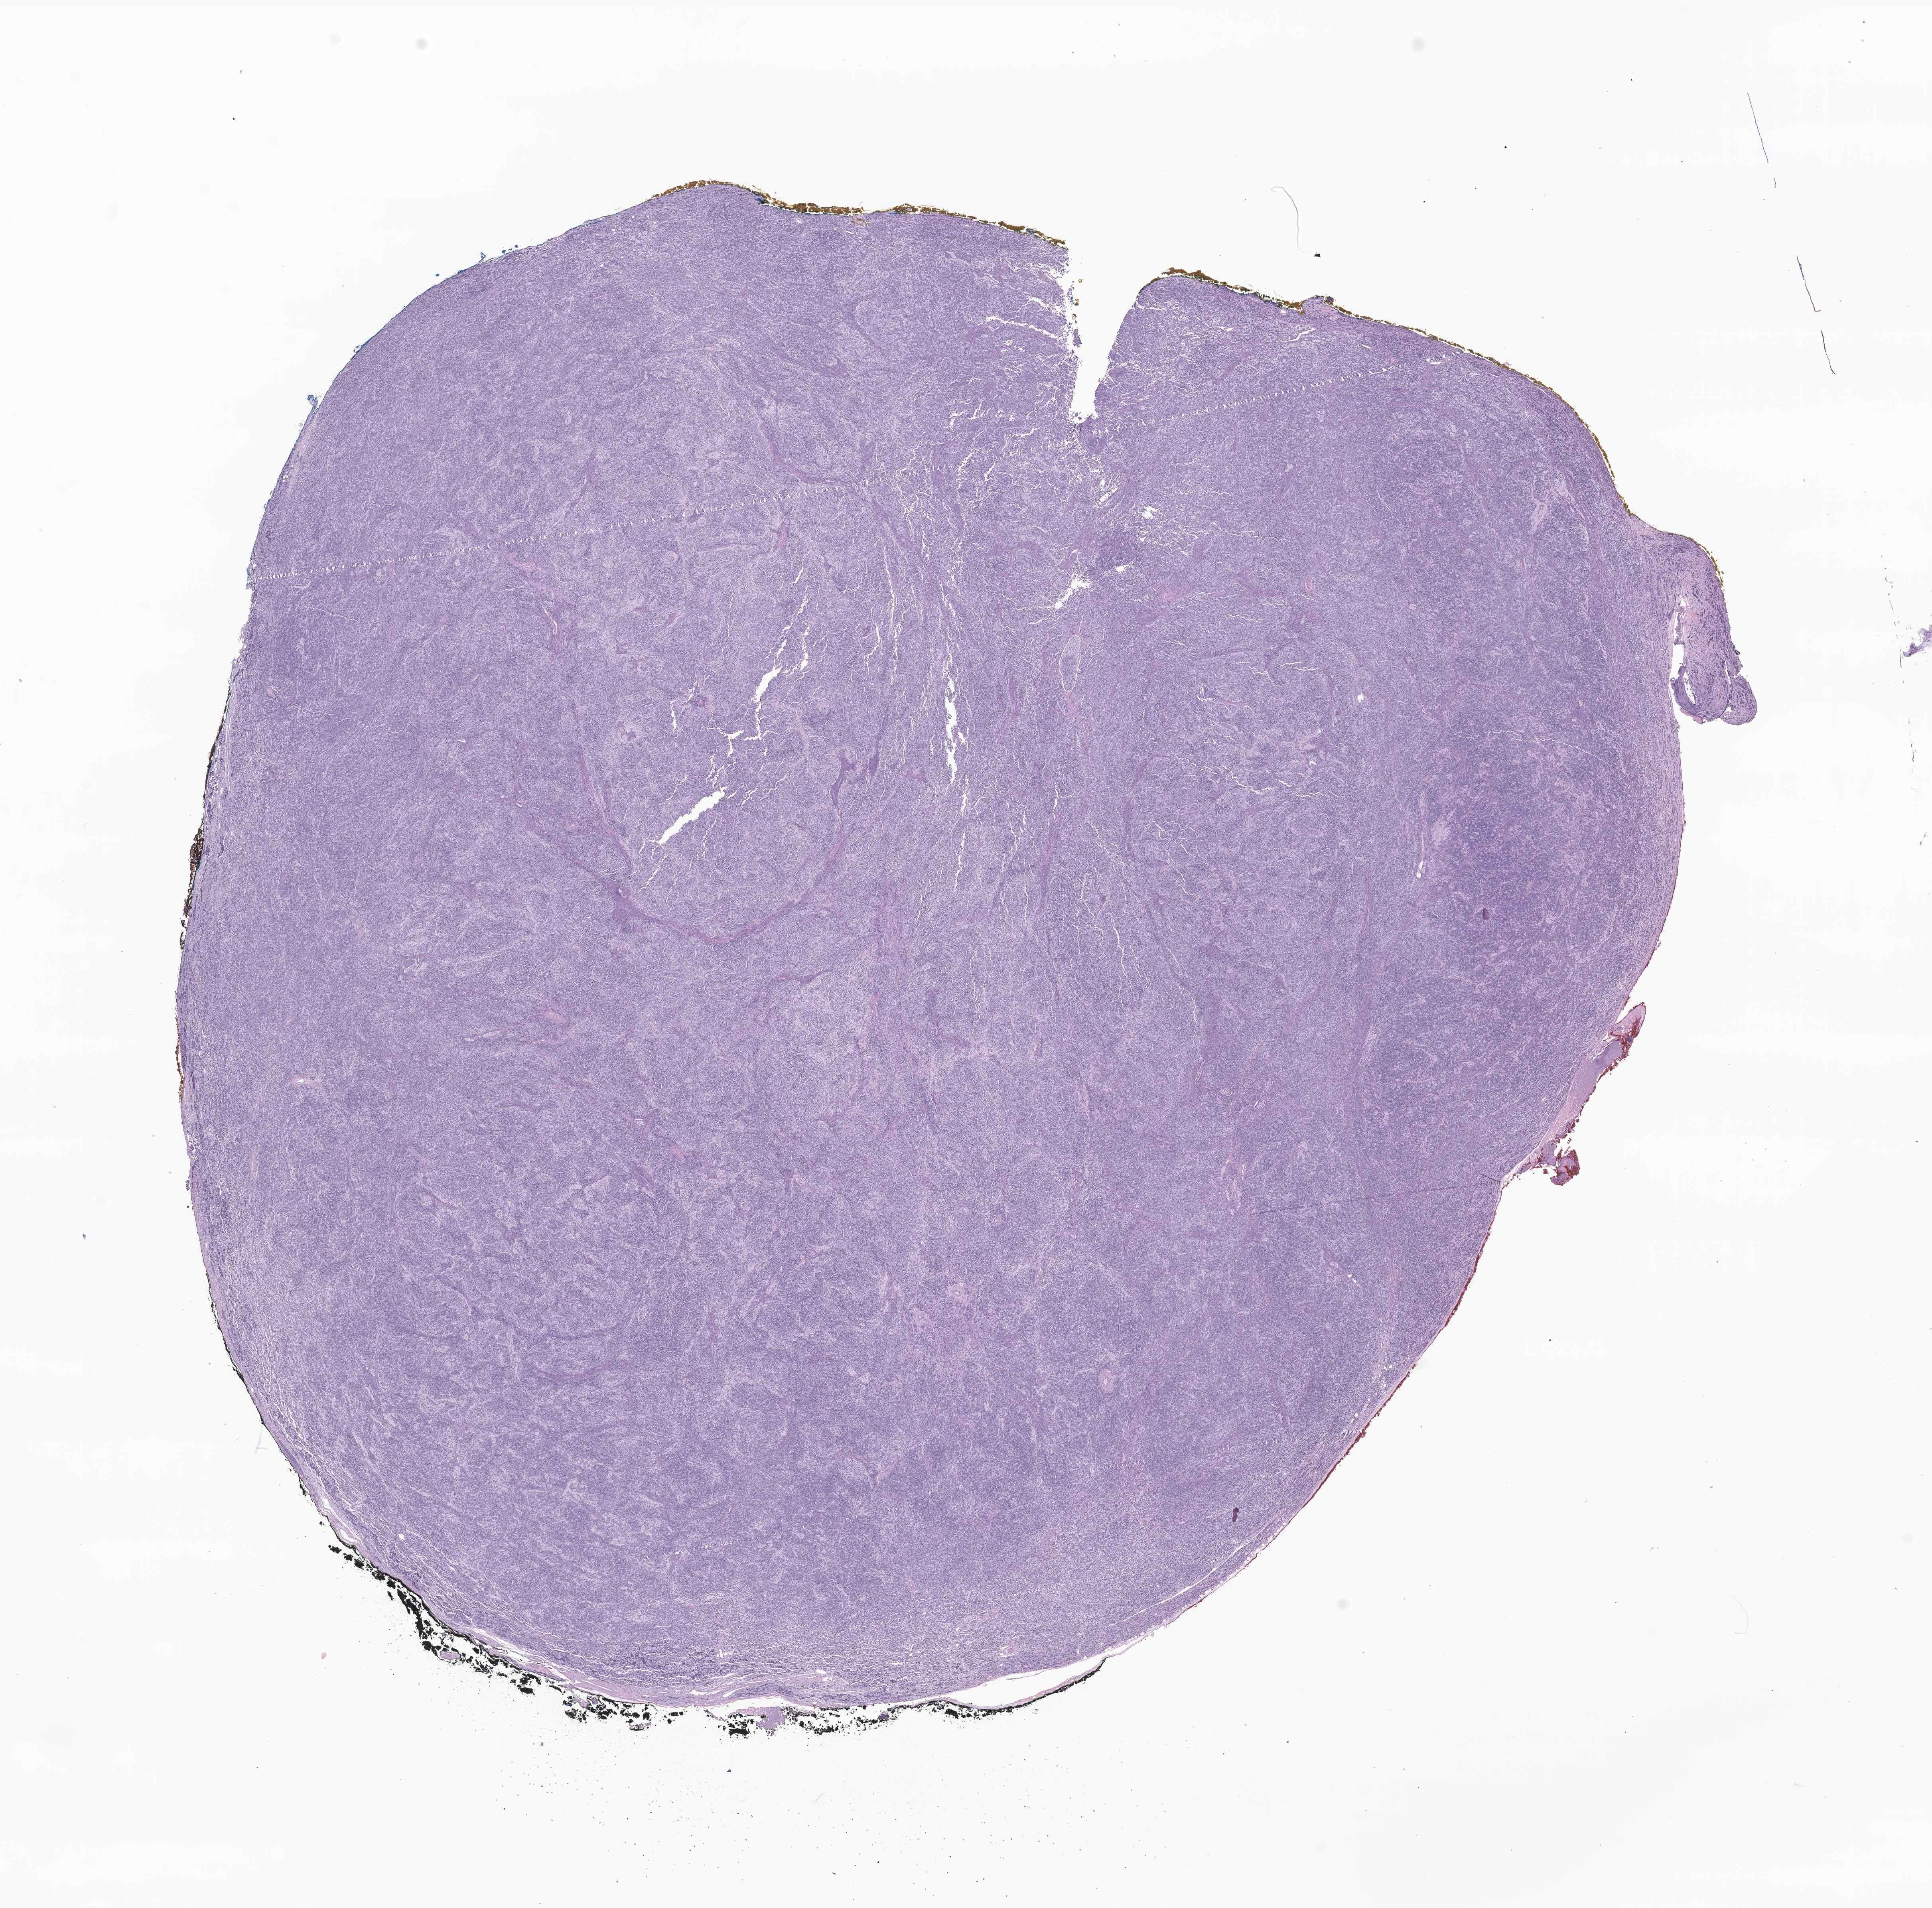
Whole-slide image, hematoxylin and eosin (H&E) stain of tumor tissue from the kidney — shown as a low-resolution overview of the whole scanned area (about 20.4 x 20.2 mm), formalin-fixed, paraffin-embedded (FFPE) tissue. Patient male; age 440 days (about 1.2 years).
- diagnosis: Neuroblastoma, NOS